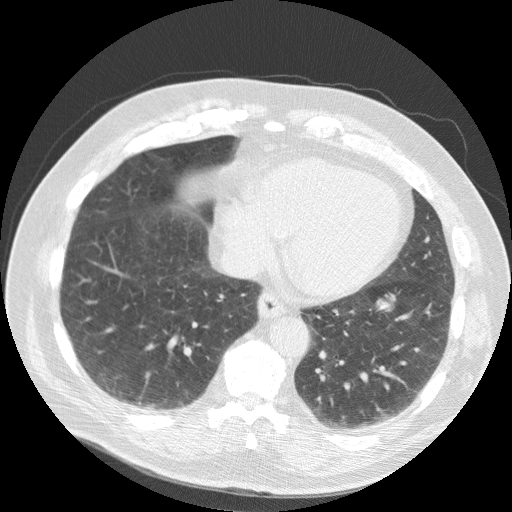
Chest CT (low-dose screening protocol), one axial image, second annual screen, lung window (W 1500 / L -600 HU), 2.5 mm slice thickness, slice 75 of 188 in the series, 512 × 512 image matrix. Male participant, aged 63 years at enrolment. Current smoker at enrolment.
- Expert-annotated lung lesion, bounding box (x1, y1, x2, y2) in pixels: (361, 287, 410, 326).
- The screening reader recorded 2 non-calcified nodules or masses ≥4 mm on this exam (right middle lobe, left lower lobe); which of them this box marks is not recorded.
- Later outcome: lung cancer diagnosed 633 days after this screen (after the third annual screen) — squamous cell carcinoma, NOS, left lower lobe, stage IB (AJCC 6th edition), 48 mm at pathology.